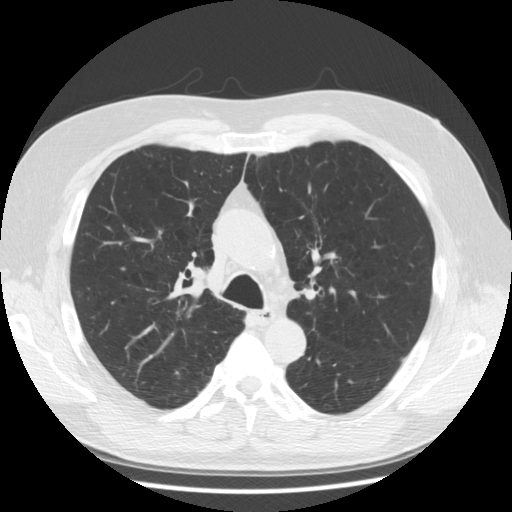
Low-dose screening chest CT, axial slice. Second screening round (one year after baseline). Lung window (W 1500 / L -600 HU). 2.5 mm slice thickness. Standard (soft-tissue) reconstruction kernel (STANDARD). 512 × 512 image matrix. Male, age 63 years at enrolment. Former smoker at enrolment.
Expert reader's lesion annotation, bounding box [x1, y1, x2, y2] px = [143, 222, 174, 248]. No non-calcified nodule or mass ≥4 mm was recorded by the screening reader at this exam. Lung cancer was diagnosed 717 days after this screen (after the third annual screen): adenocarcinoma, NOS, right upper lobe, stage IIA (AJCC 6th edition), 8 mm at pathology.